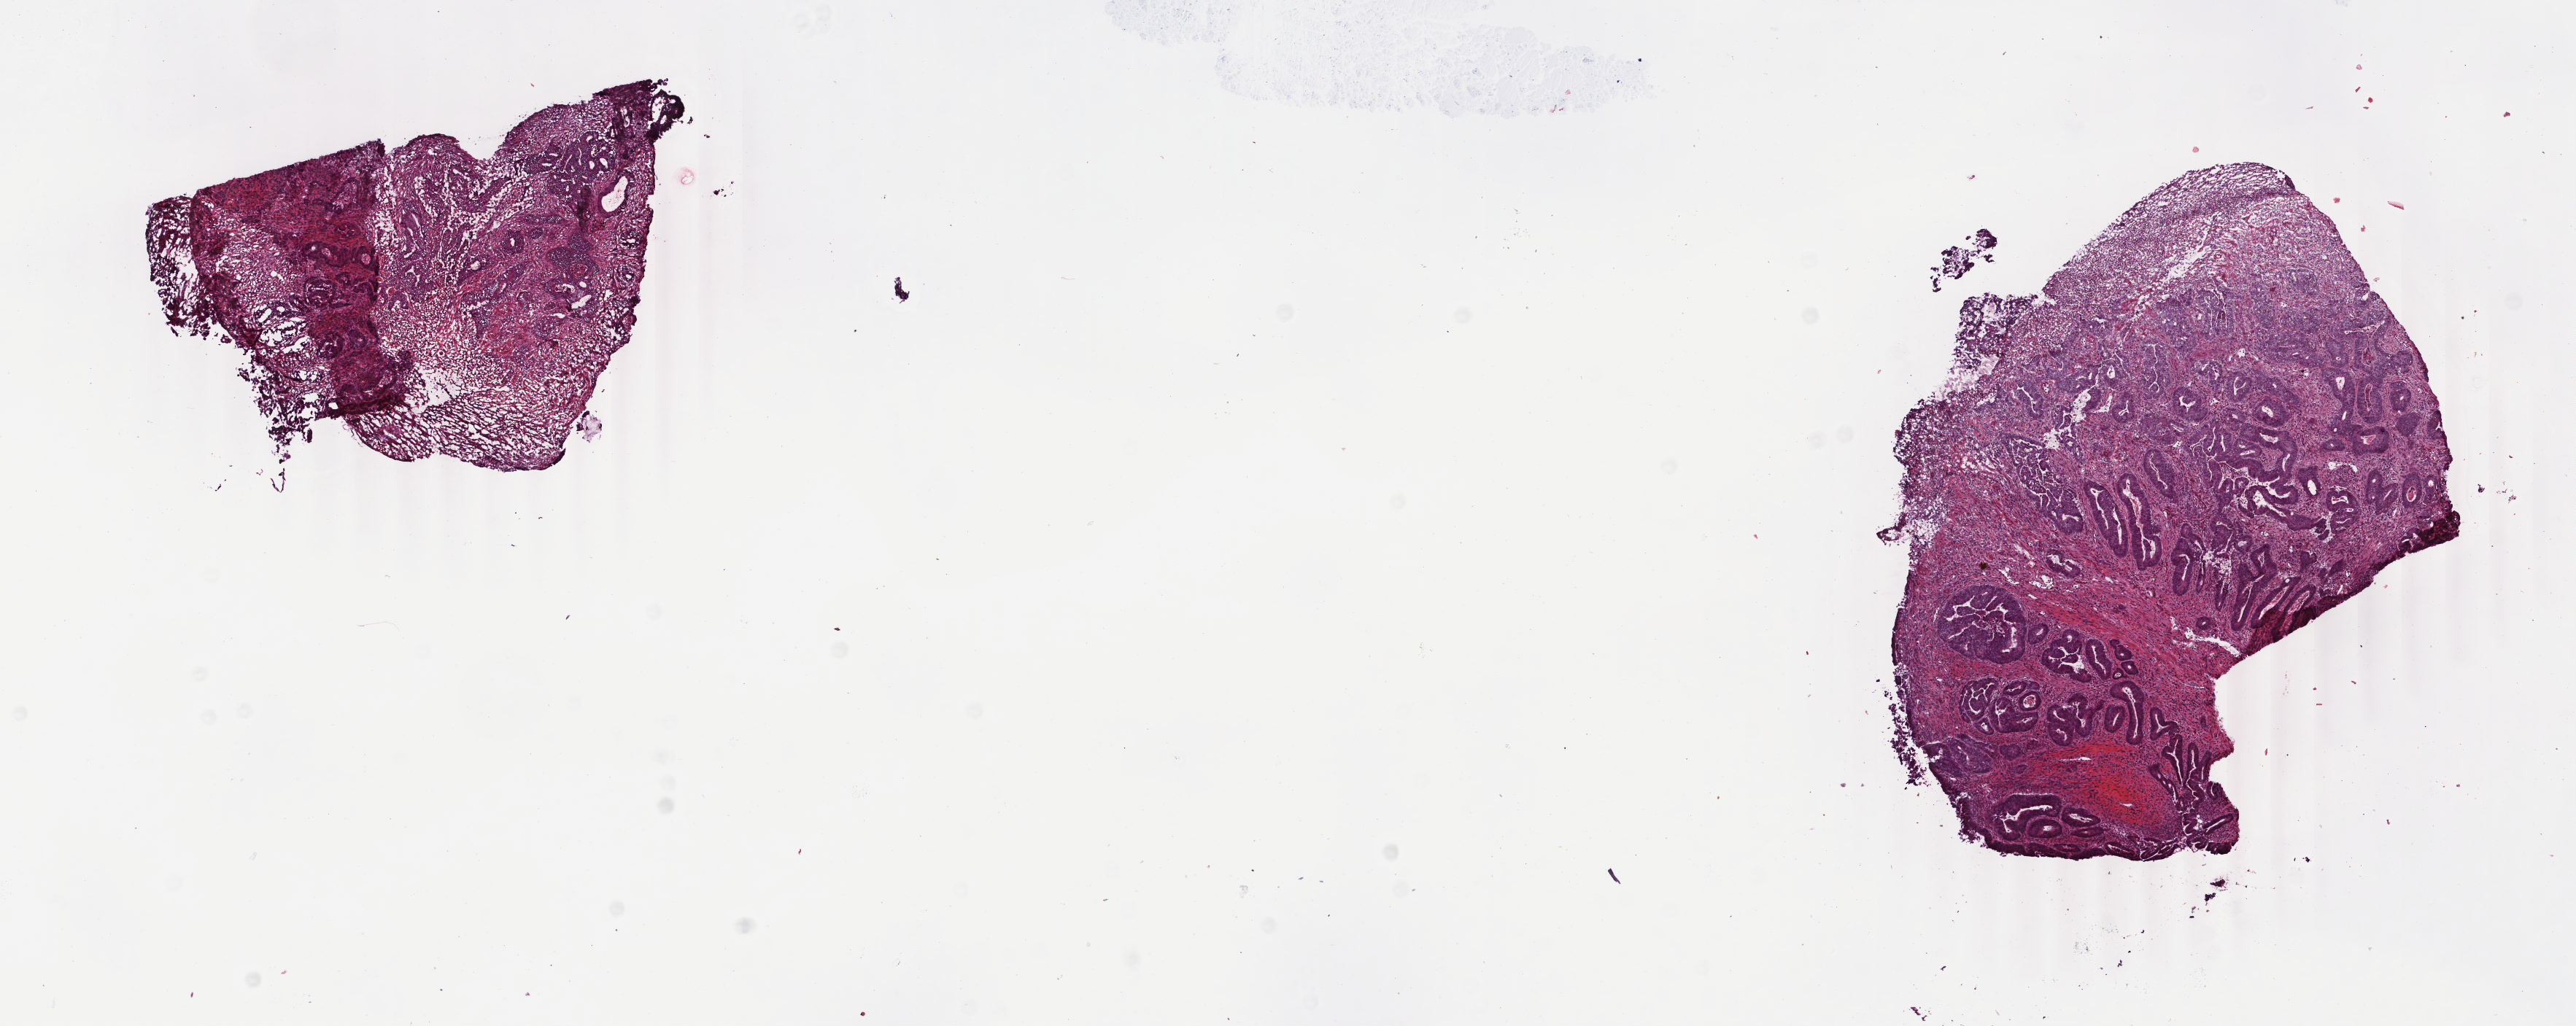
Whole-slide histology image, H&E, shown as a low-resolution overview of the whole scanned area (about 14.0 x 5.6 mm, acquisition: 40x scan); frozen section from the top of the tissue portion; primary tumour sample from the colon. Female patient; age at initial diagnosis 57 years. Slide review estimates, as recorded: tumour cells 75%, tumour nuclei 65%, normal cells 0%, stromal cells 15%, necrosis 10%. Inflammatory infiltration, as recorded: lymphocyte infiltration 4%, monocyte infiltration 4%, neutrophil infiltration 20%.
* pathologic diagnosis: Adenocarcinoma, NOS (sigmoid colon)
* AJCC pathologic stage: IIA